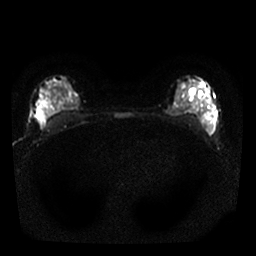
Breast MRI, one axial slice; position 17 of 25 along the scan axis; diffusion-weighted series; image 2 of 4 stored at this slice position (different b-values; order by instance number); 1.5 T; 4 mm slice thickness; 256 × 256 image matrix. Female patient.
Structures marked on this image (manually delineated by an expert):
- tumour on diffusion-weighted imaging: bounding box <37,107,46,128> (left, top, right, bottom; pixels)